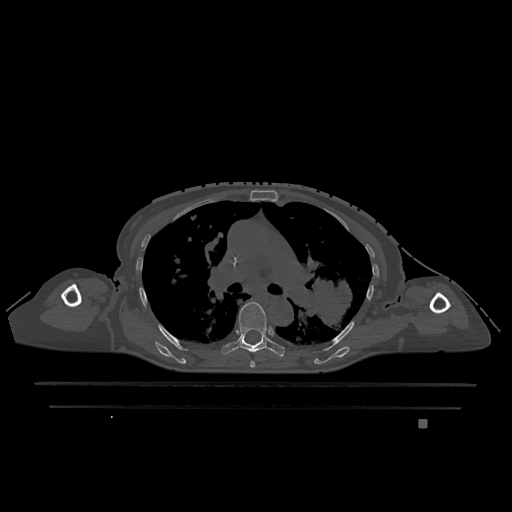
CT including the spine, one axial slice. Slice 795 of 1317 in the series (ordered by position). Bone window (W 1800 / L 400 HU). 0.5 mm slice thickness. 512 × 512 image matrix, field of view 500 × 500 mm. Female patient, age 74 years. From the clinical record (not read from this slice): primary cancer: lung; vertebrae with lytic lesions (as recorded): T1, T4, T5, T6, L4, L5.
Annotated regions visible in this slice (semi-automatically segmented with operator editing):
- T5 vertebra: bounding box <250,361,255,368> (left, top, right, bottom; pixels)
- T6 vertebra: <221,302,285,357>